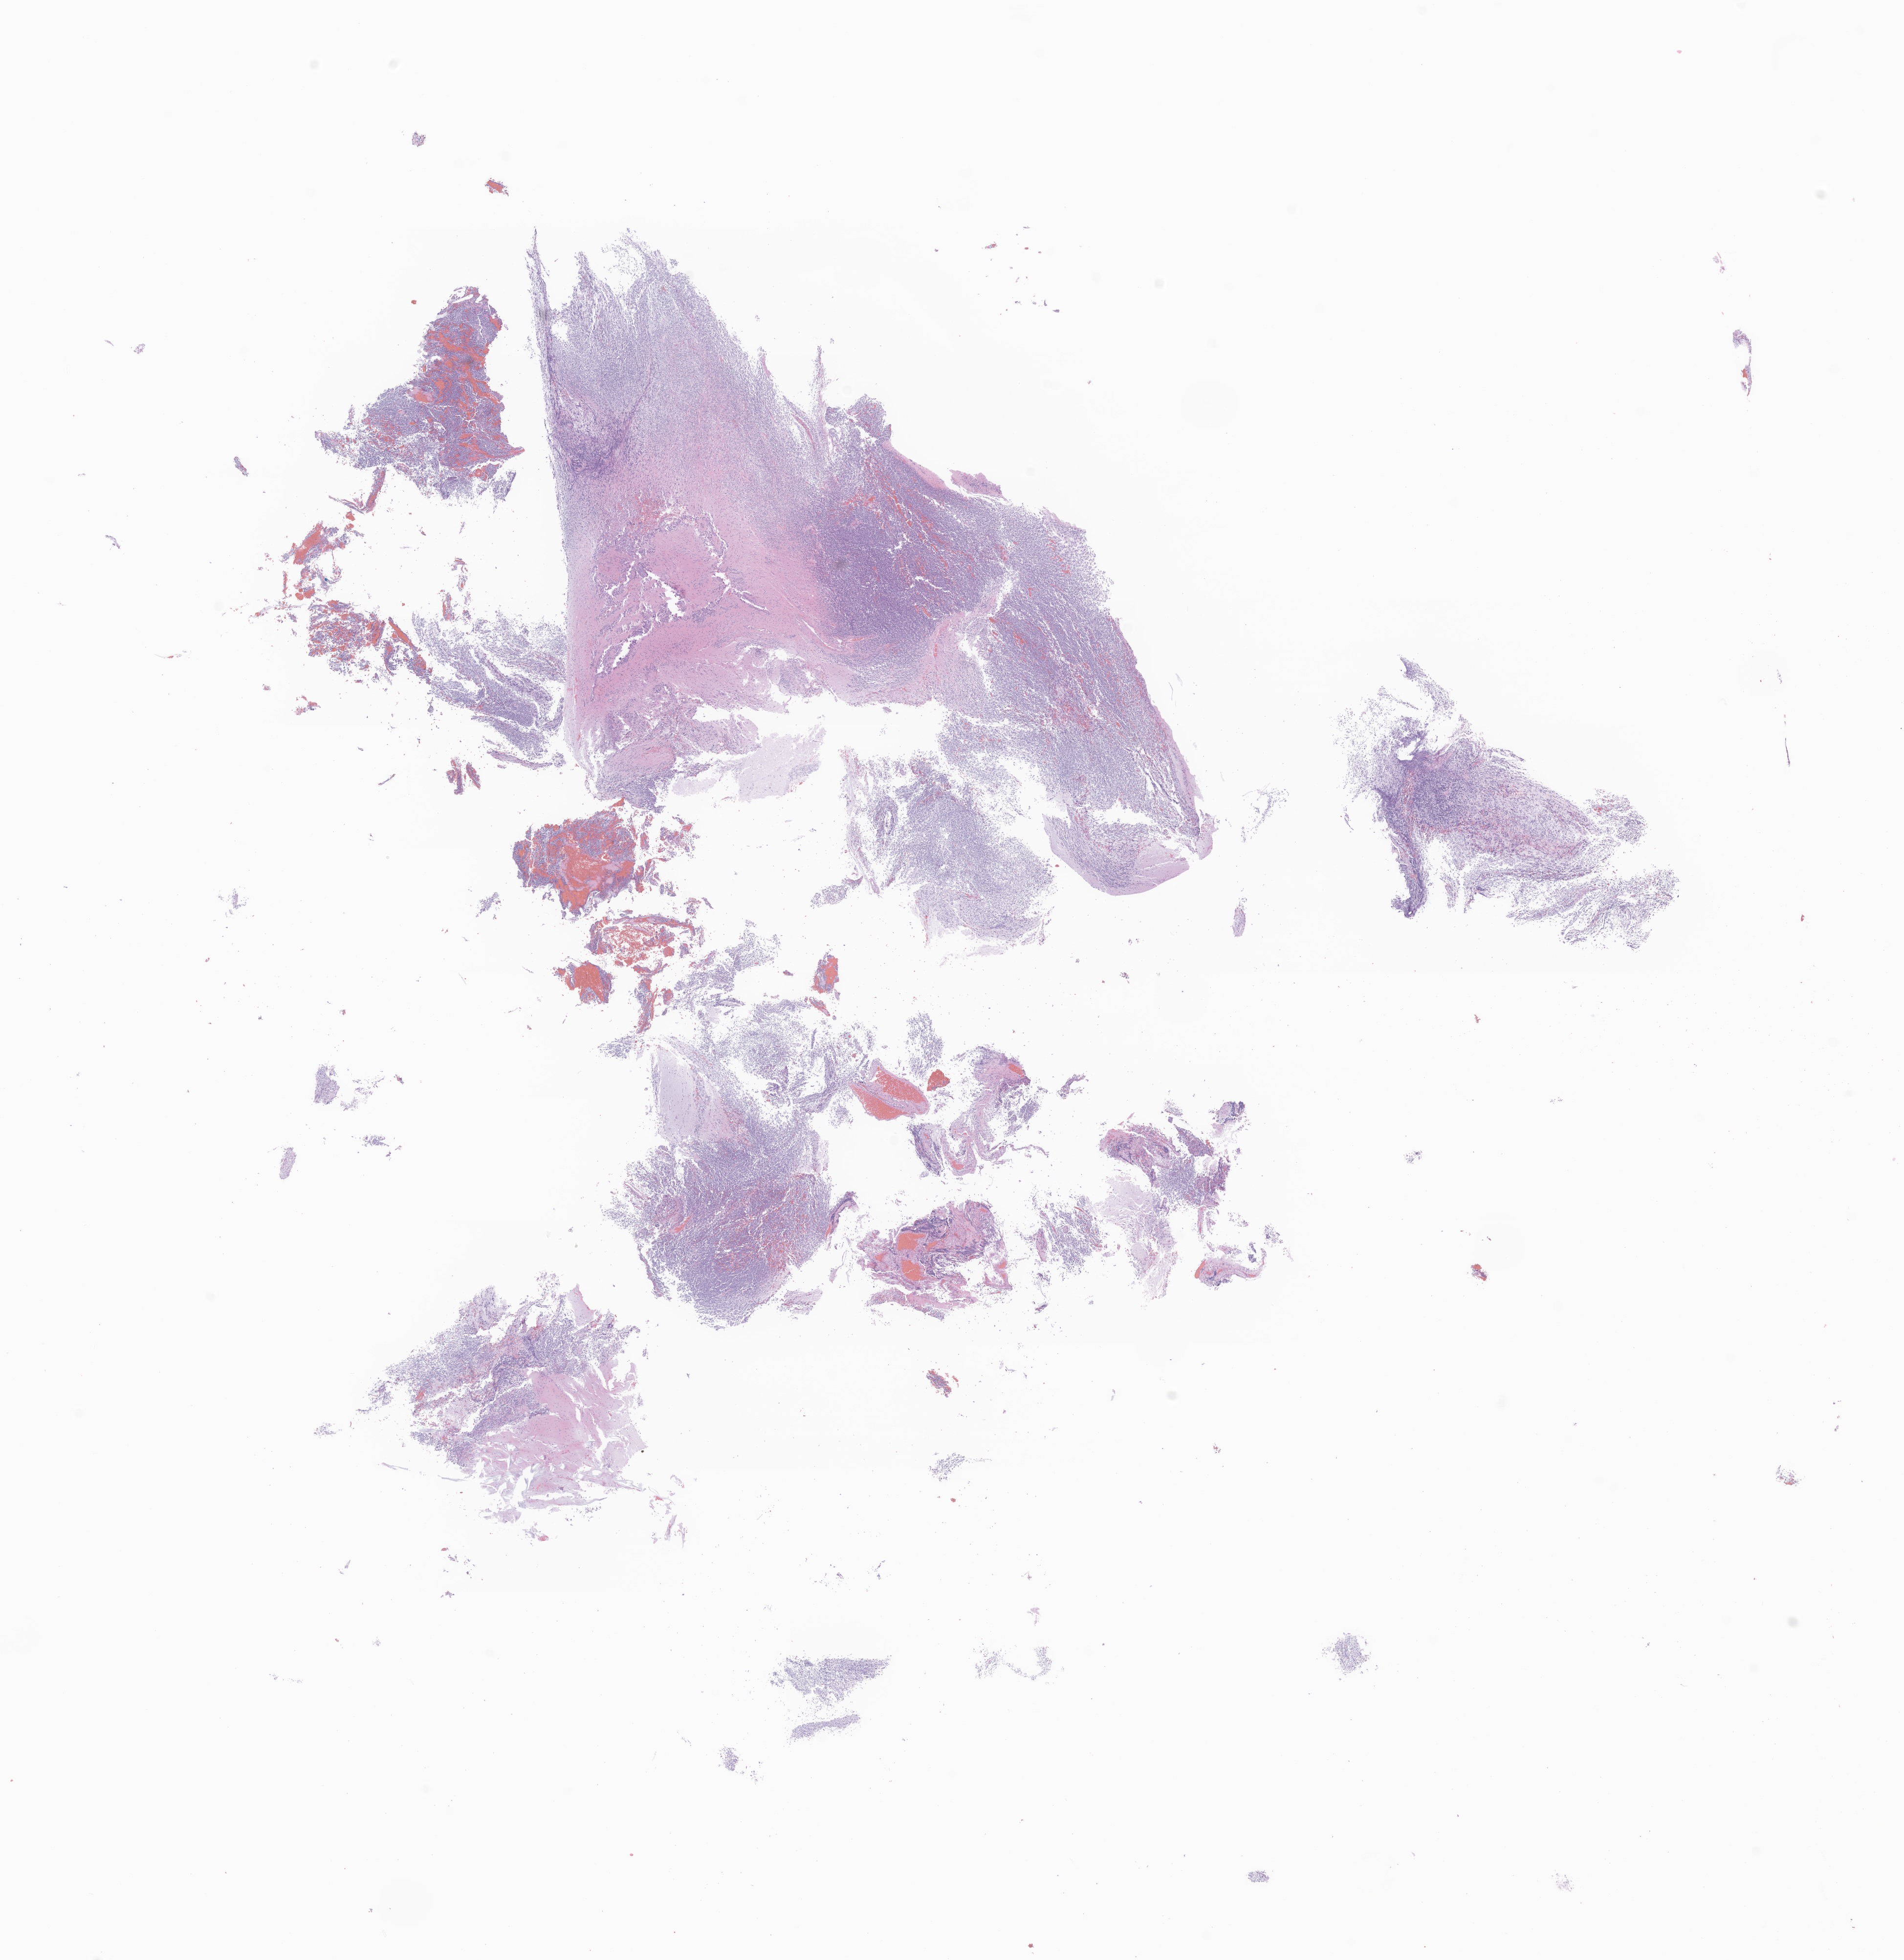
Whole-slide image, H&E stain of tumor tissue from the brain — shown as a low-resolution overview of the whole scanned area (about 16.4 x 16.9 mm). Formalin-fixed paraffin-embedded section. Male patient, age 88 months (7 years 4 months).
Recorded diagnosis: Medulloblastoma, NOS.